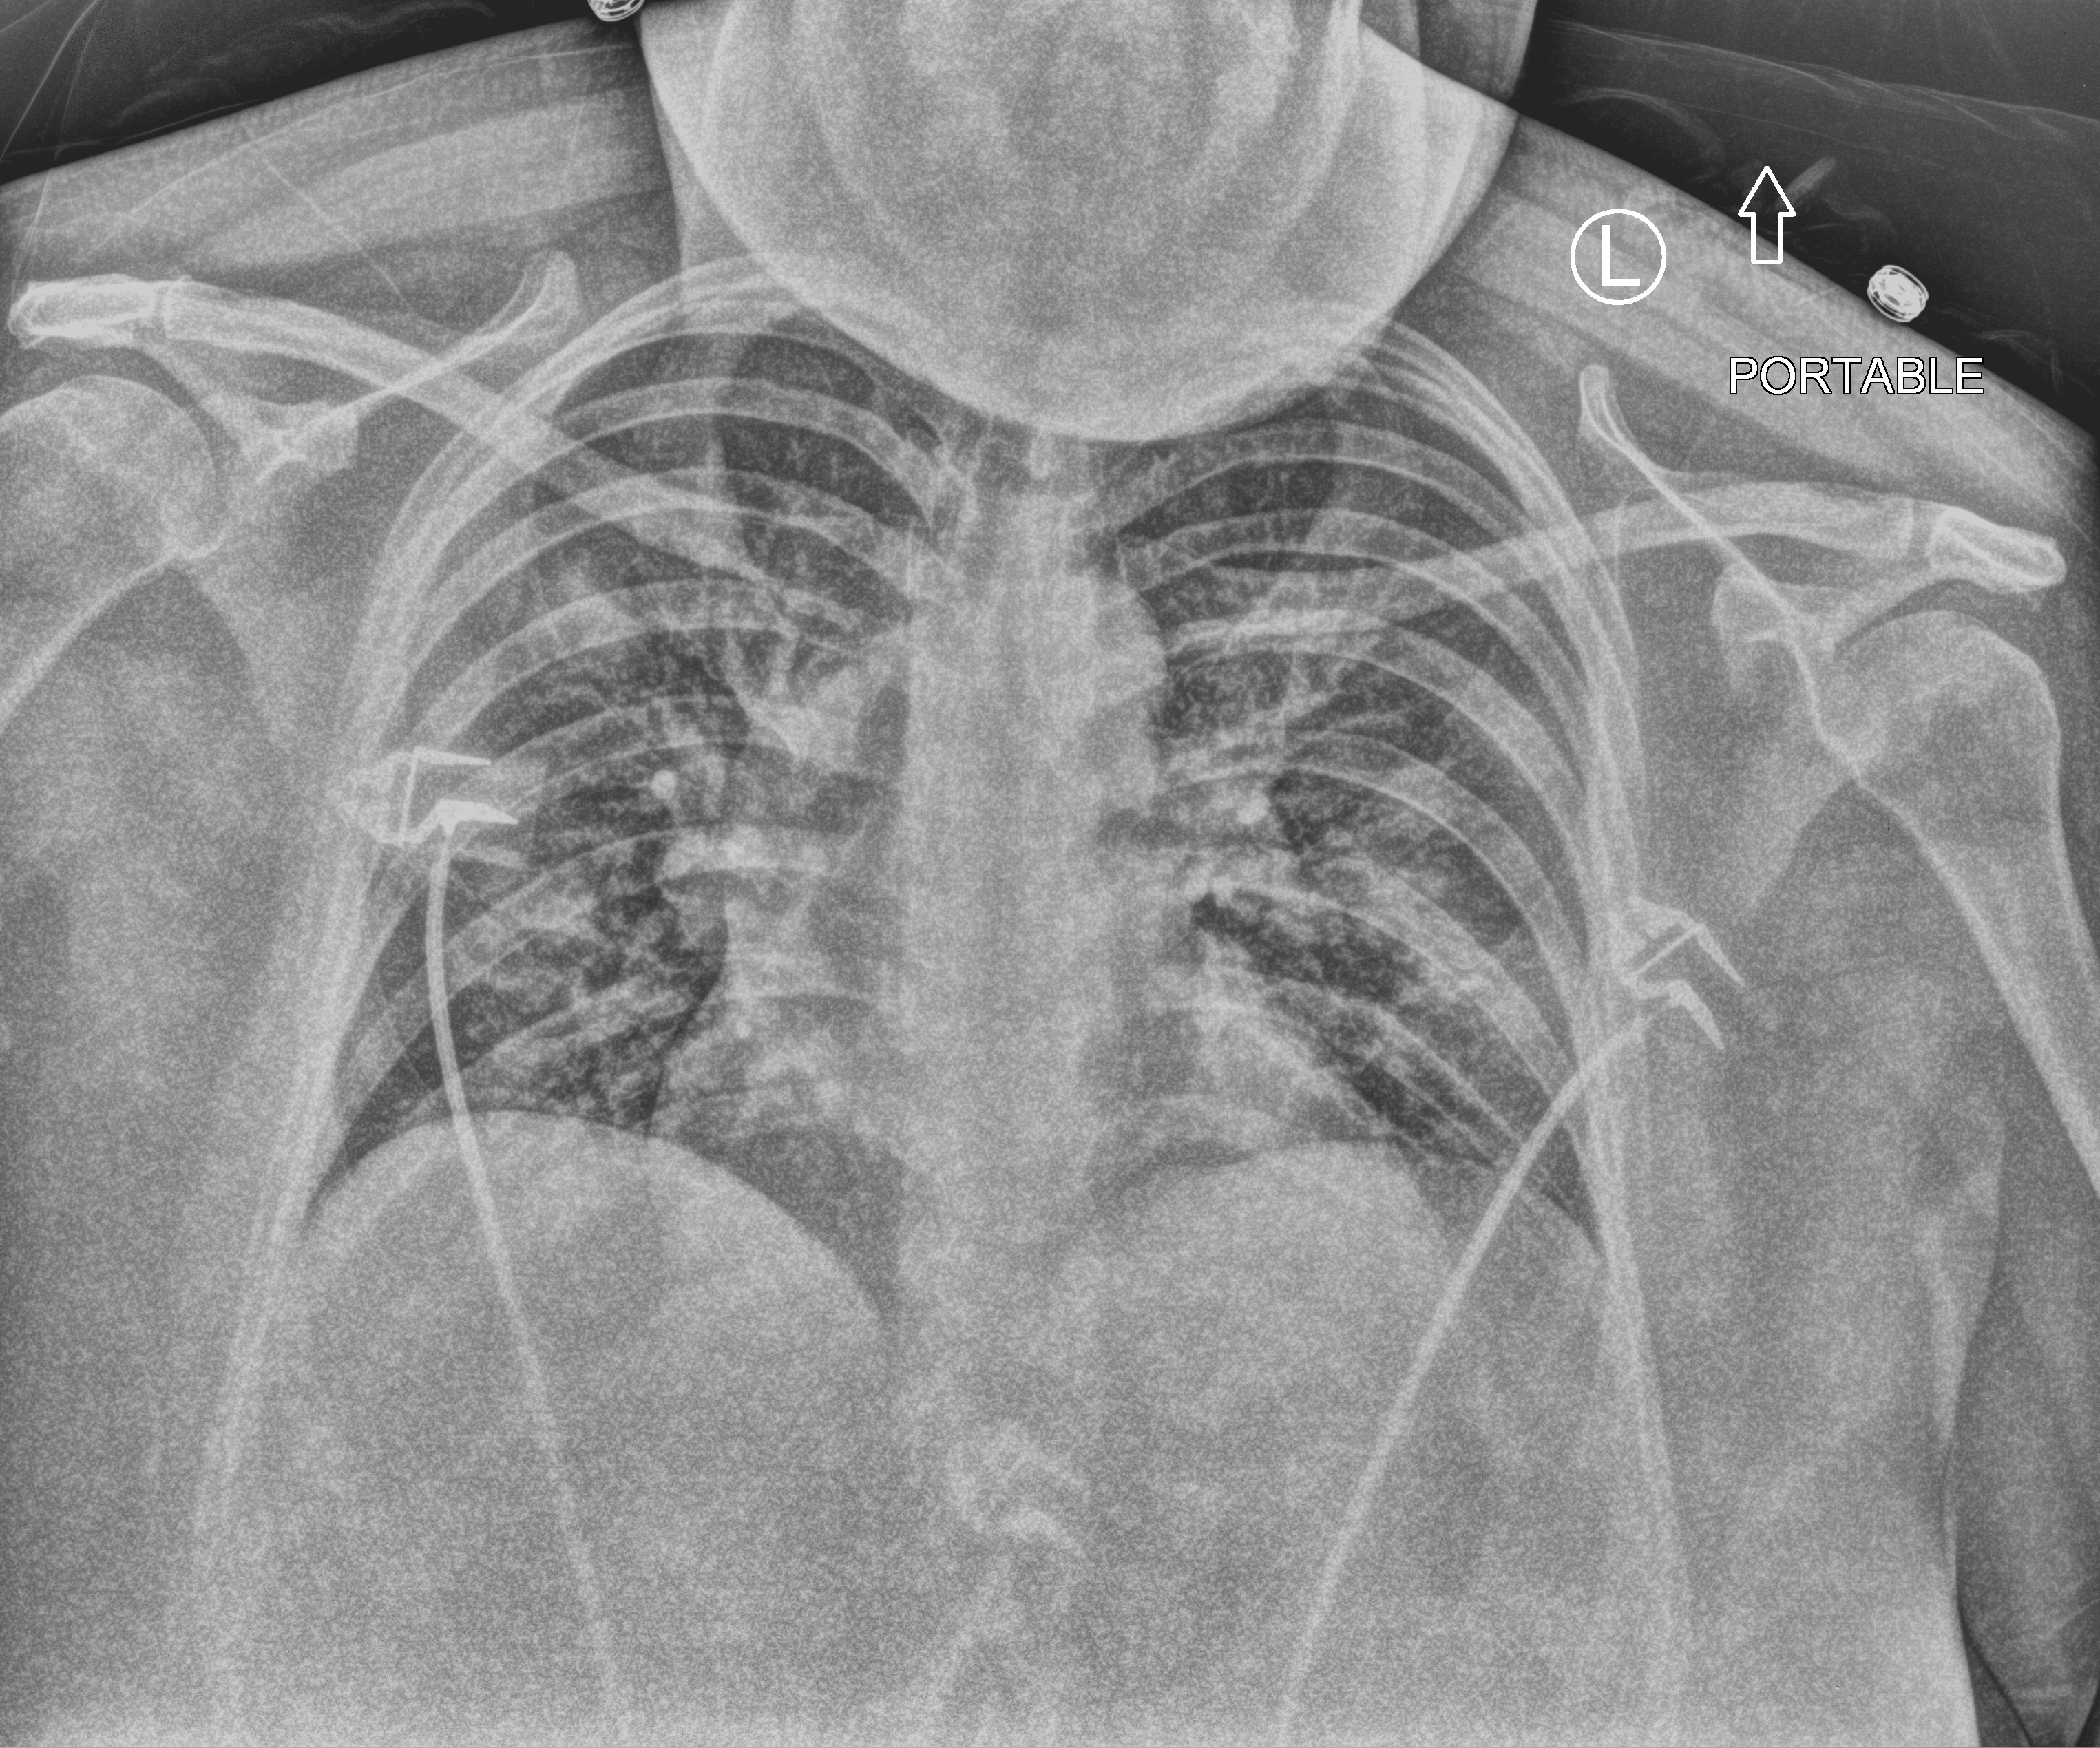
Portable chest radiograph; anteroposterior (AP) projection. Patient hospitalised with COVID-19; female, aged 18–59 years.
From the hospital-stay record, not from the radiograph (when in the stay this image was taken is not recorded):
- admitted to intensive care during this hospital stay: no